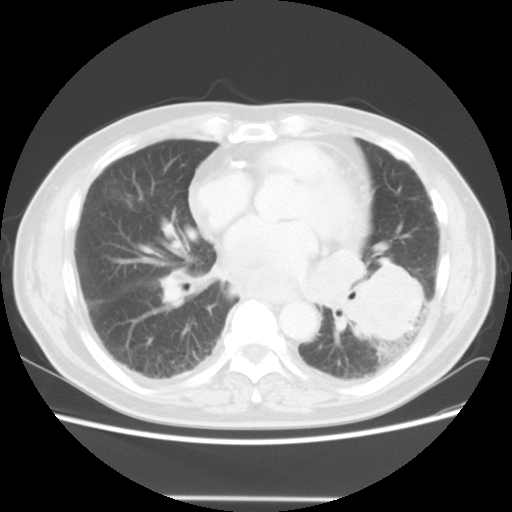
Chest CT, one axial slice; position 21 of 56 along the scan axis; reconstruction kernel STANDARD; lung window (W 1500 / L -600 HU); 5 mm slice thickness; 512 × 512 image matrix, field of view 360 × 360 mm. Male patient, age 66 years. From the clinical record (not read from this slice): clinical TNM (as recorded): T4 N3 M0.
Annotated regions visible in this slice (rectangle marked by the reading radiologist):
- lung tumour (recorded histology: small cell carcinoma): box from (x=341, y=245) to (x=422, y=353) px